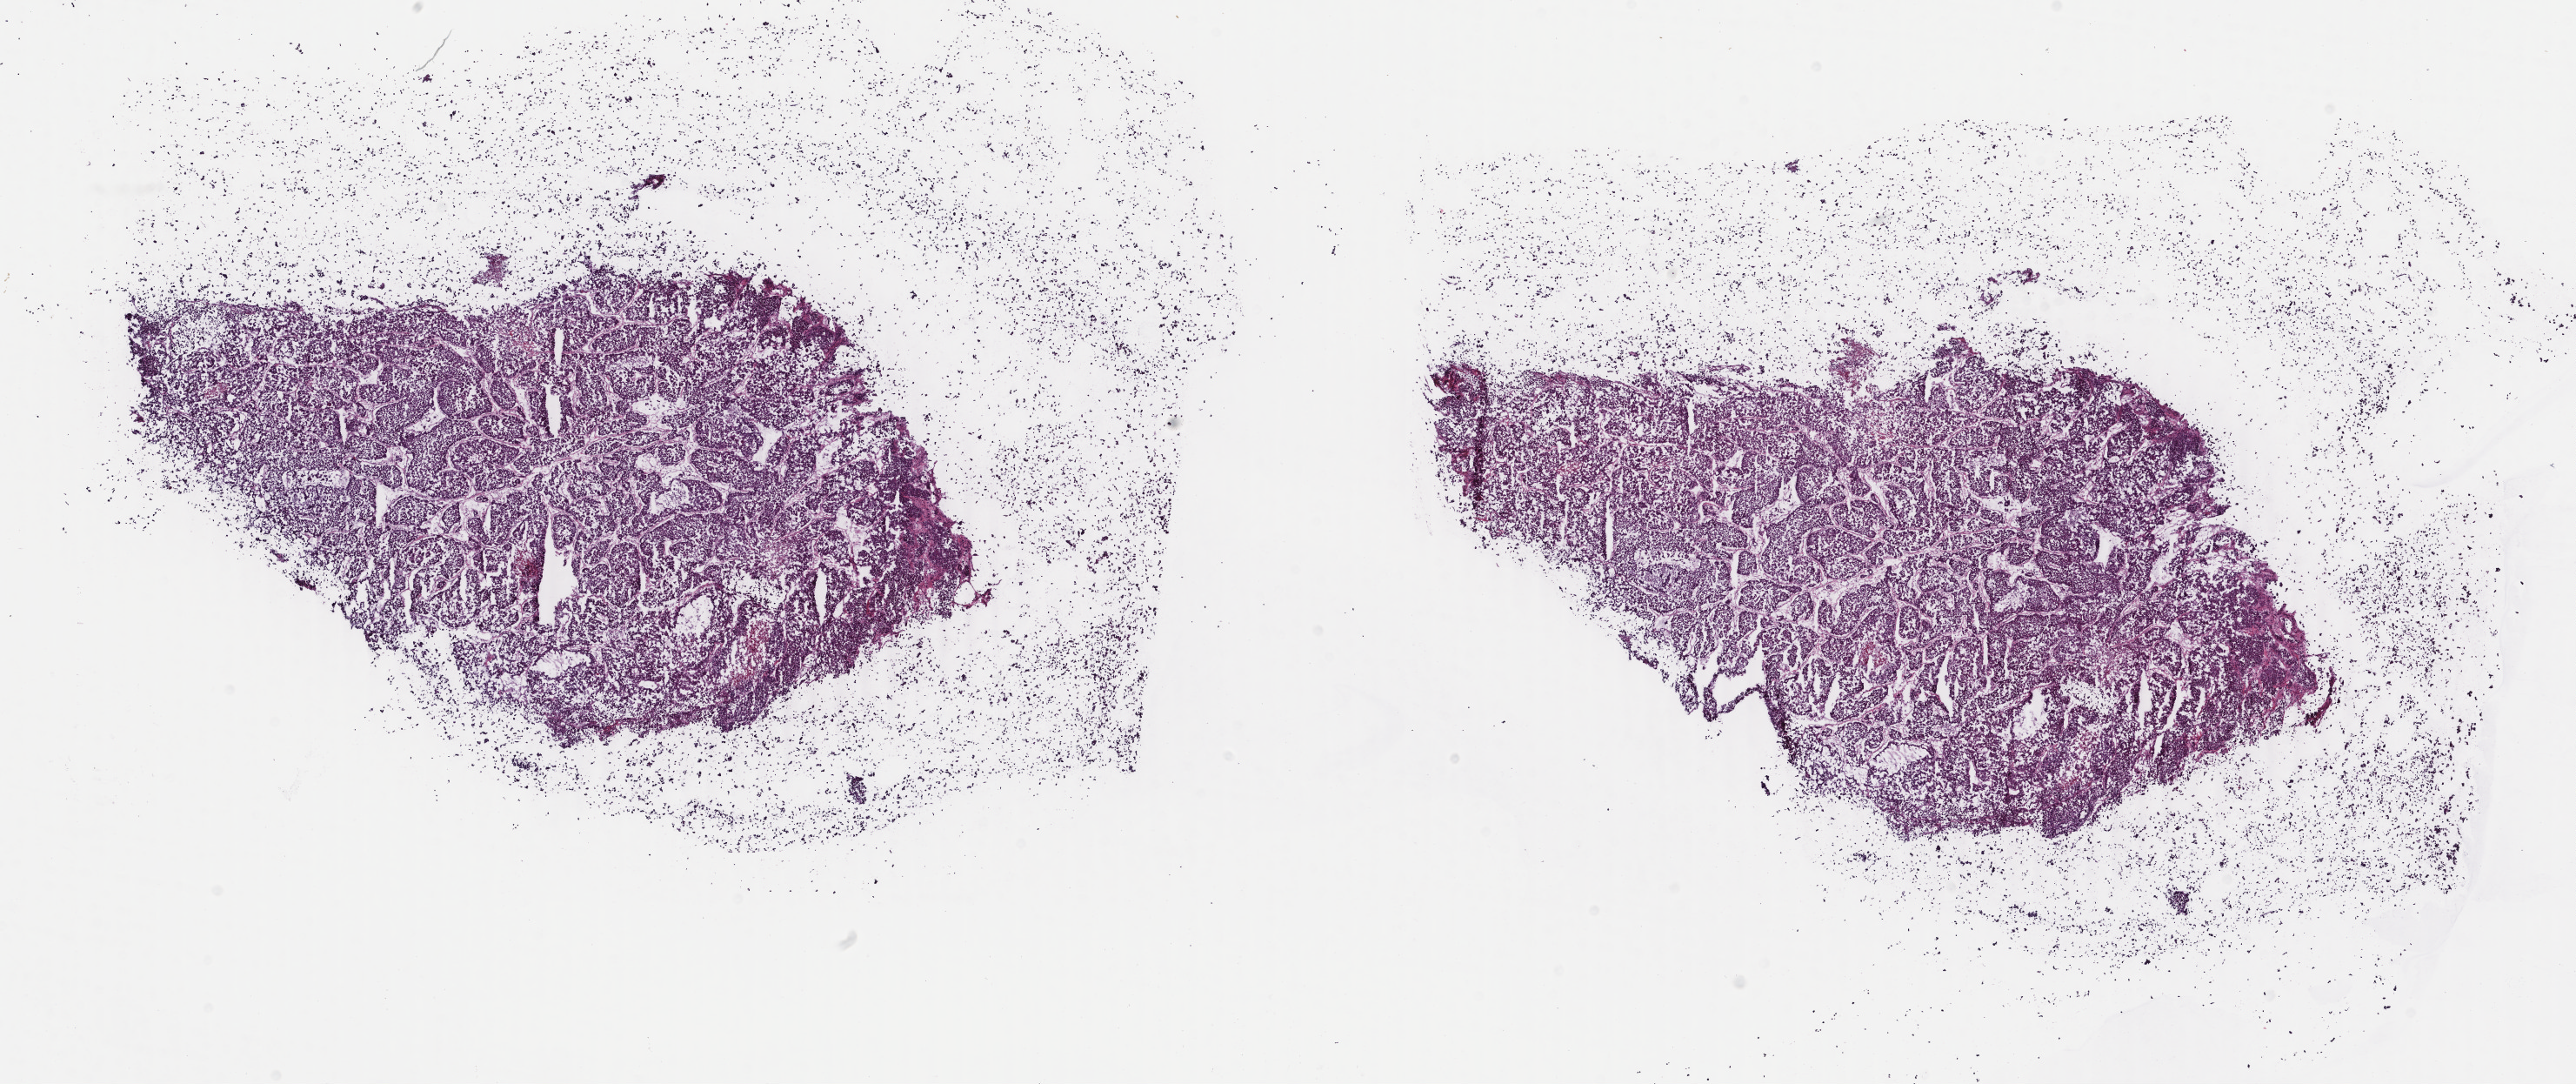
H&E whole-slide image, a low-resolution overview of the entire scanned area, about 23.6 x 9.9 mm (from a 40x scan). Frozen section from the bottom of the tissue portion. Sample: primary tumour, liver. Male, age 69 years at initial diagnosis. Histologic grade: G2 (moderately differentiated). Pathologist review of this section (percent, as recorded): tumour cells 96%, tumour nuclei 95%, normal cells 0%, stromal cells 0%, necrosis 4%. Infiltration values recorded for this section: lymphocyte infiltration 0%, monocyte infiltration 0%, neutrophil infiltration 0%.
Histologic diagnosis: Hepatocellular carcinoma, NOS.